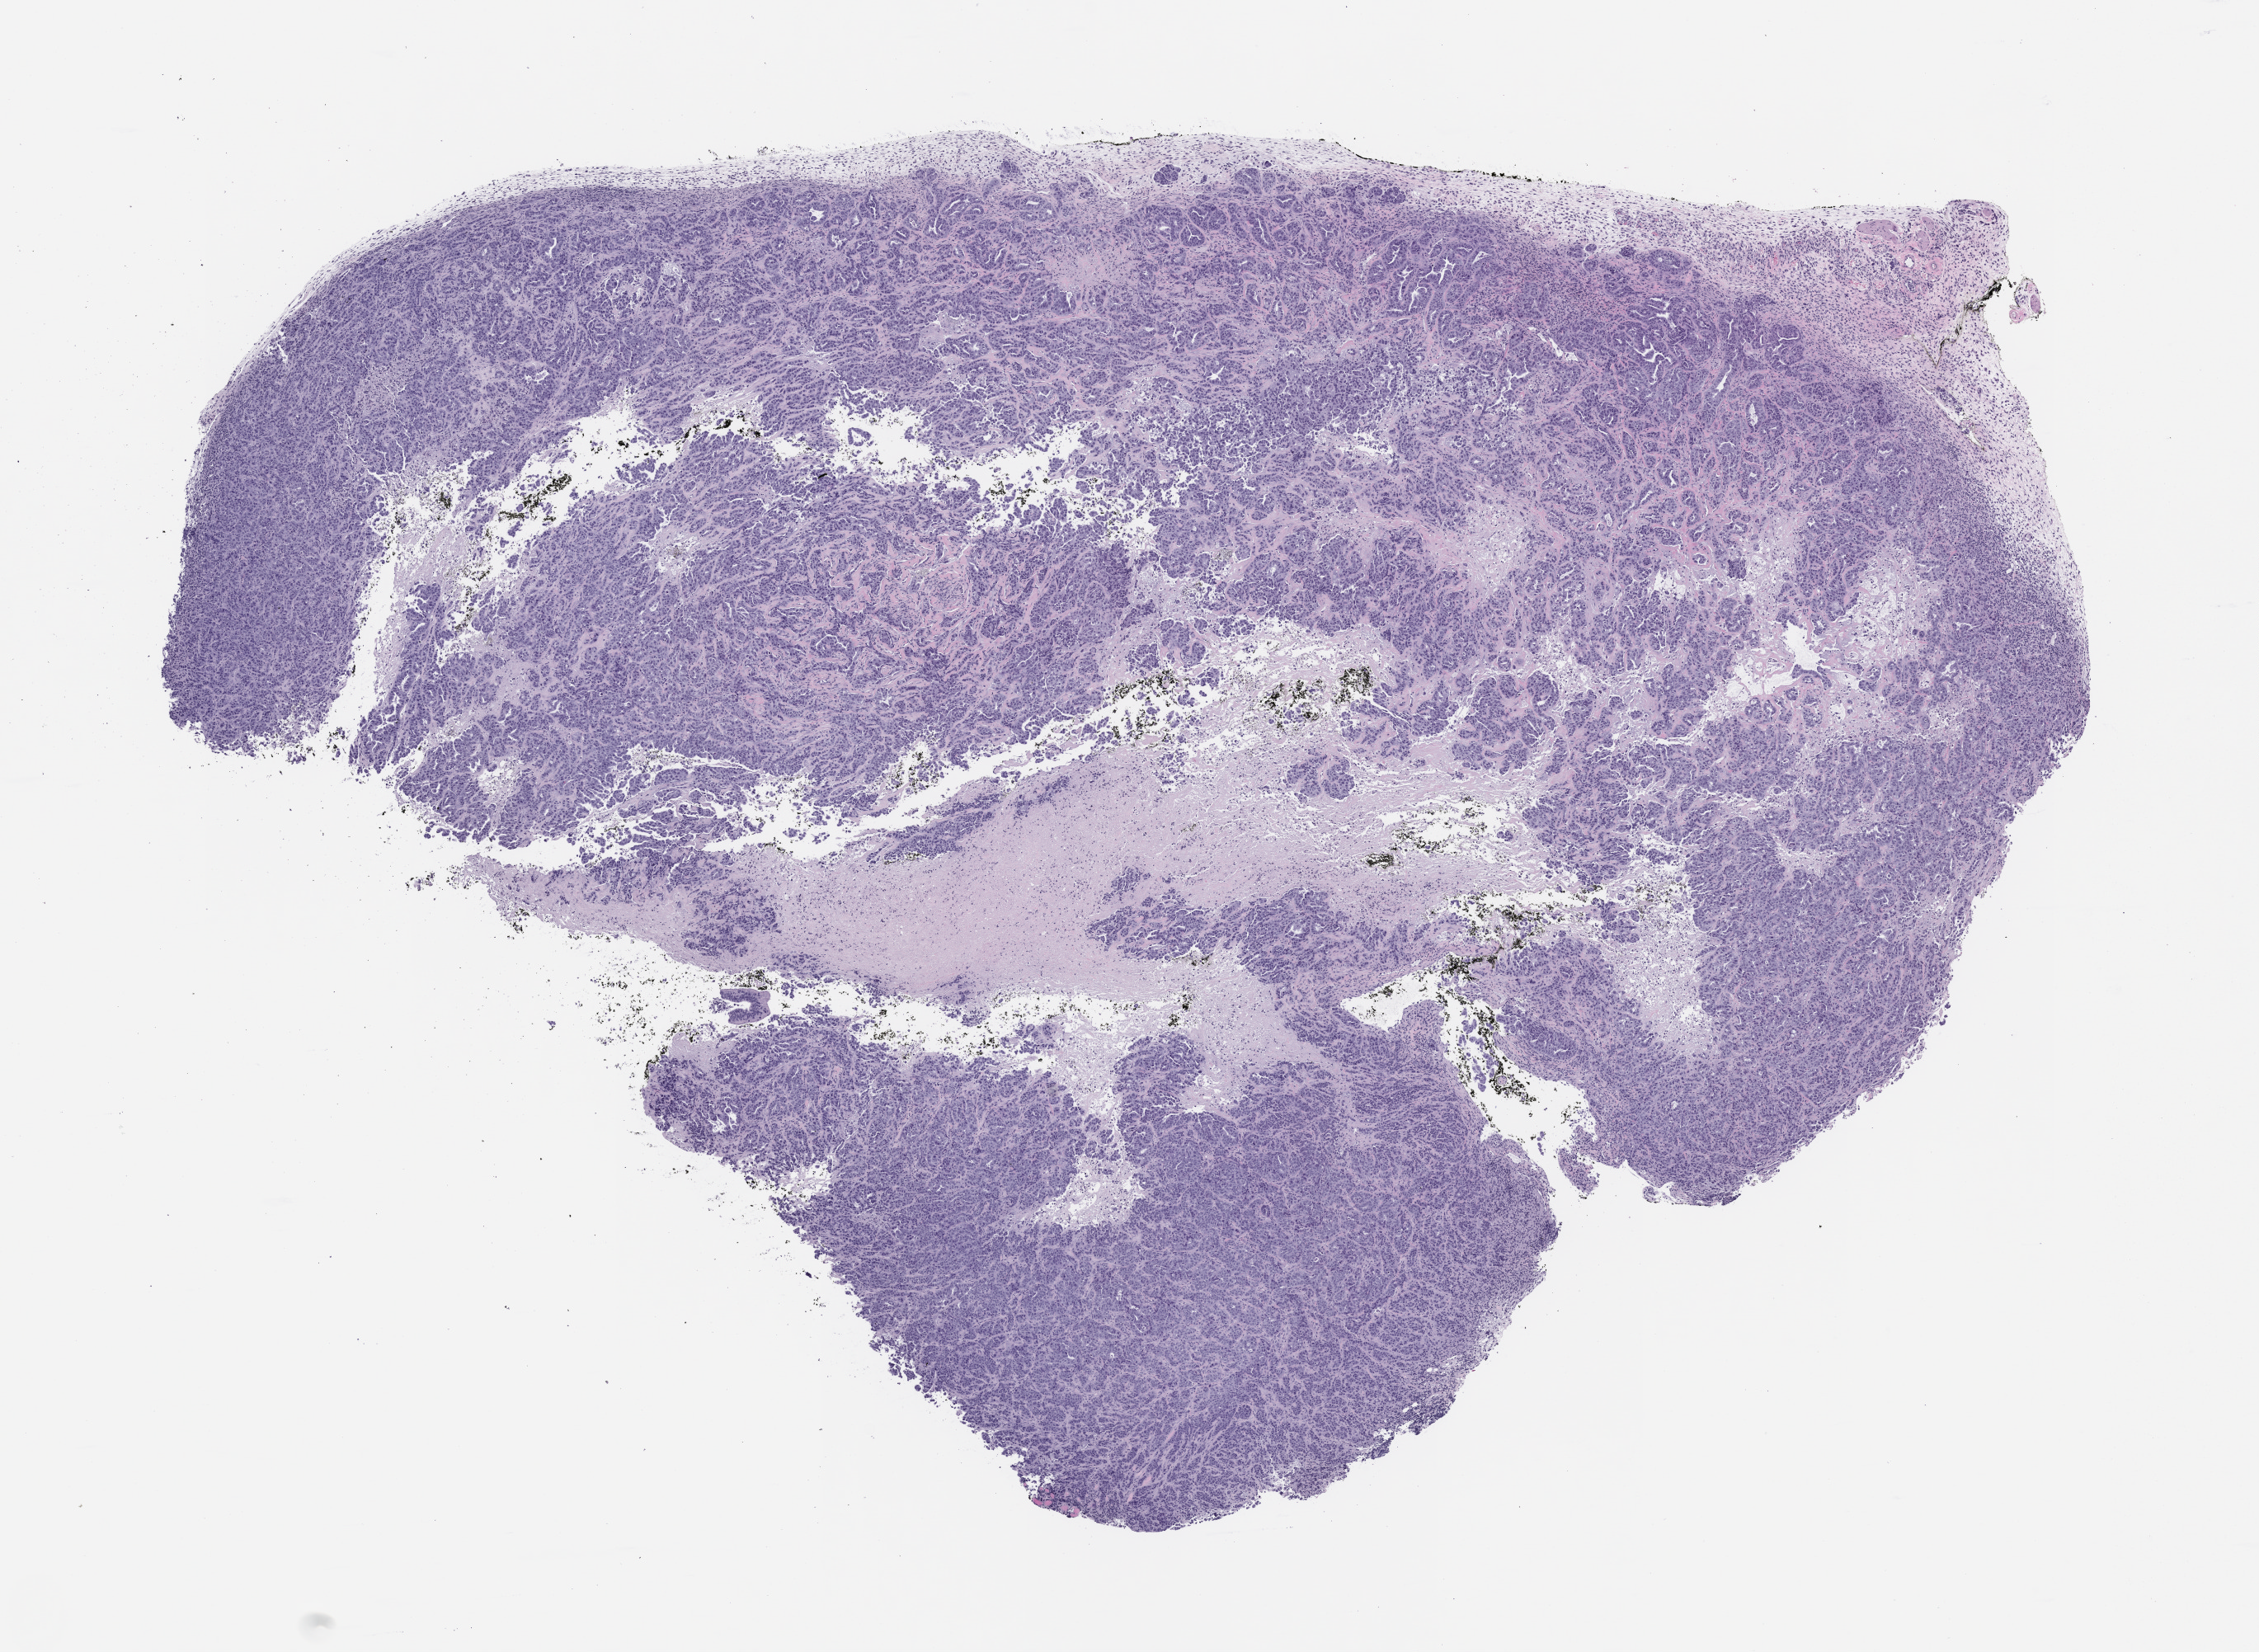
Haematoxylin and eosin whole-slide image of a patient-derived xenograft (PDX) tumor grown in a mouse — low-resolution overview of the scanned area, about 11.0 x 8.1 mm, formalin-fixed, paraffin-embedded (FFPE) tissue, originating tumor site category: lung.
- originating patient diagnosis: Lung Adenocarcinoma